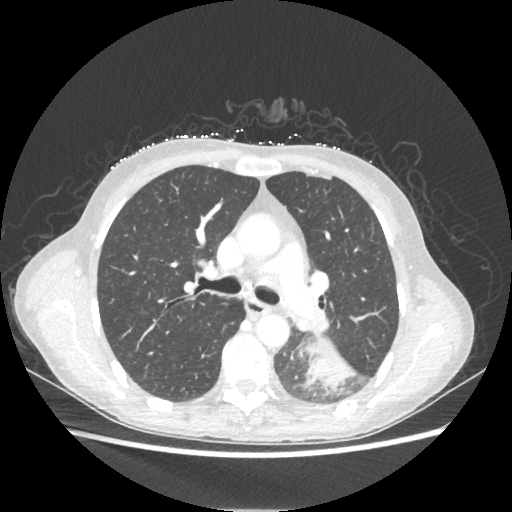
Chest CT, one axial slice; slice 134 of 221 in the series (ordered by position); reconstruction kernel STANDARD; lung window (W 1500 / L -600 HU); 1.25 mm slice thickness; 512 × 512 image matrix, field of view 360 × 360 mm. Female patient, age 53 years. From the clinical record (not read from this slice): clinical TNM (as recorded): T3 N0 M0.
Outlined on this slice (bounding box drawn by a radiologist):
- lung tumour (recorded histology: adenocarcinoma): bounding box <304,339,355,390> (left, top, right, bottom; pixels)